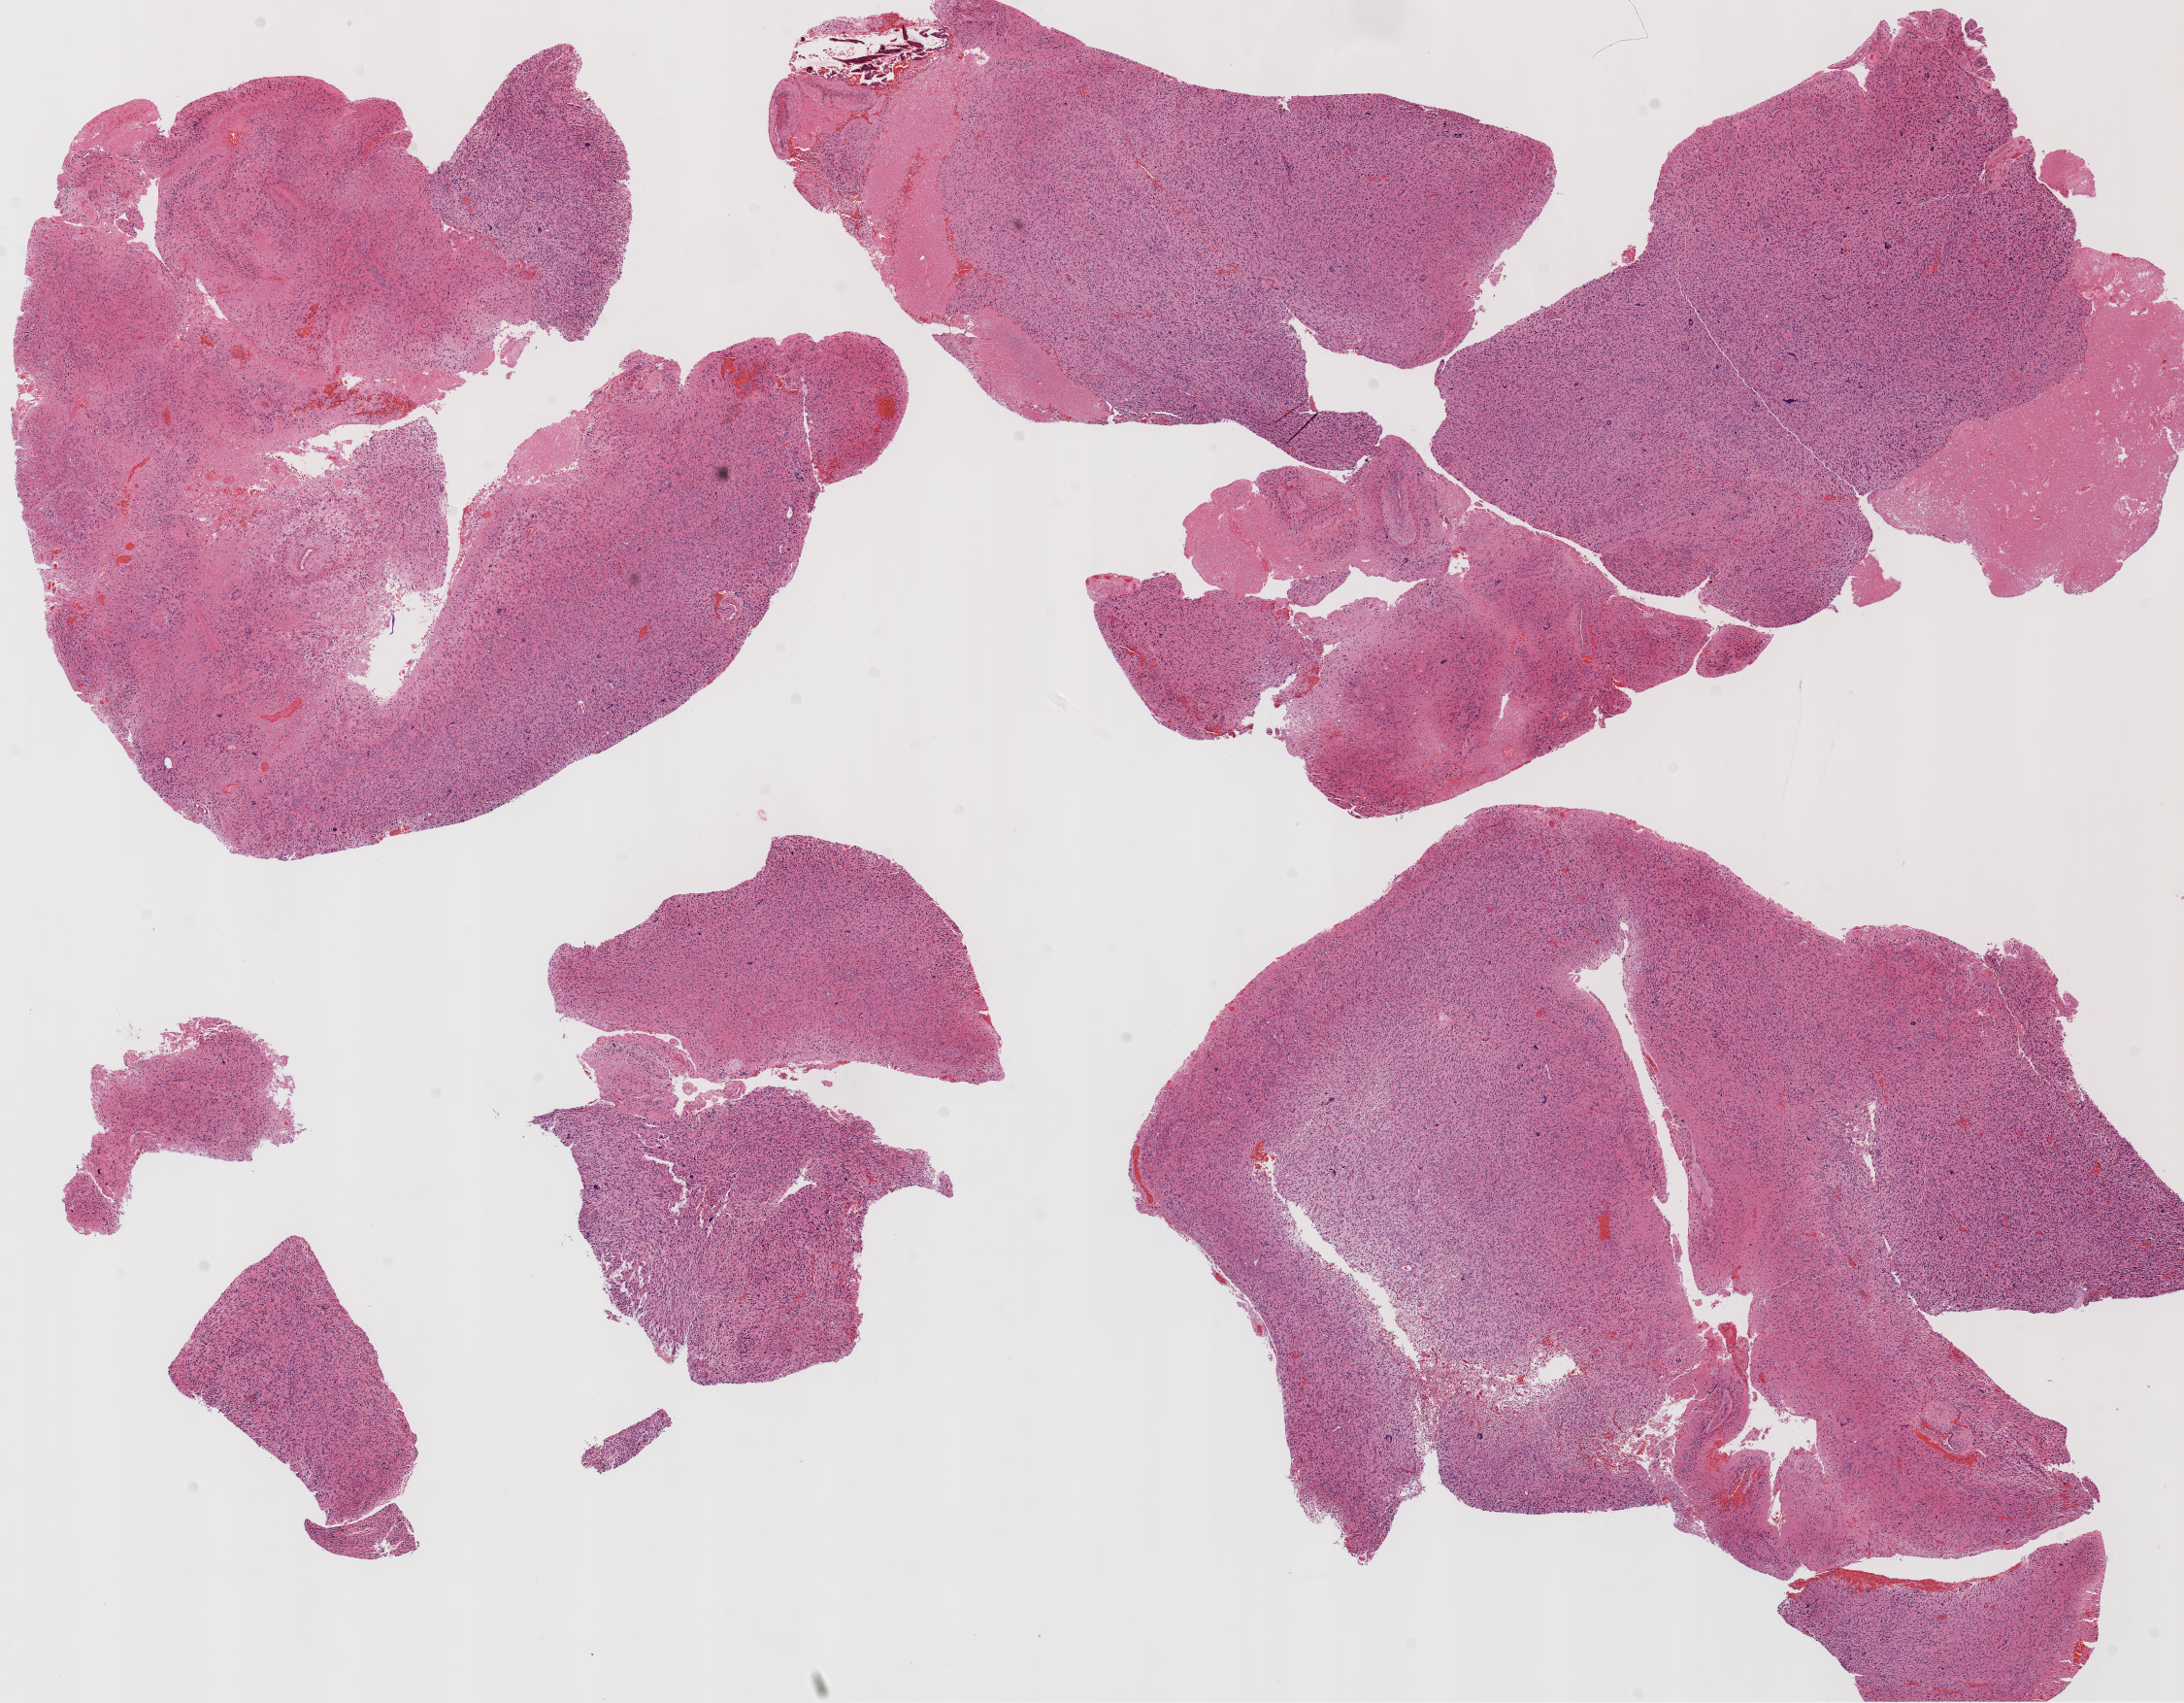
H&E whole-slide image, whole scanned area (about 18.1 x 14.1 mm, acquisition: 20x scan) shown as a low-resolution overview; formalin-fixed paraffin-embedded (FFPE) diagnostic section; primary tumour sample from the brain. Male patient; age at initial diagnosis 69 years.
Diagnosis: Glioblastoma.